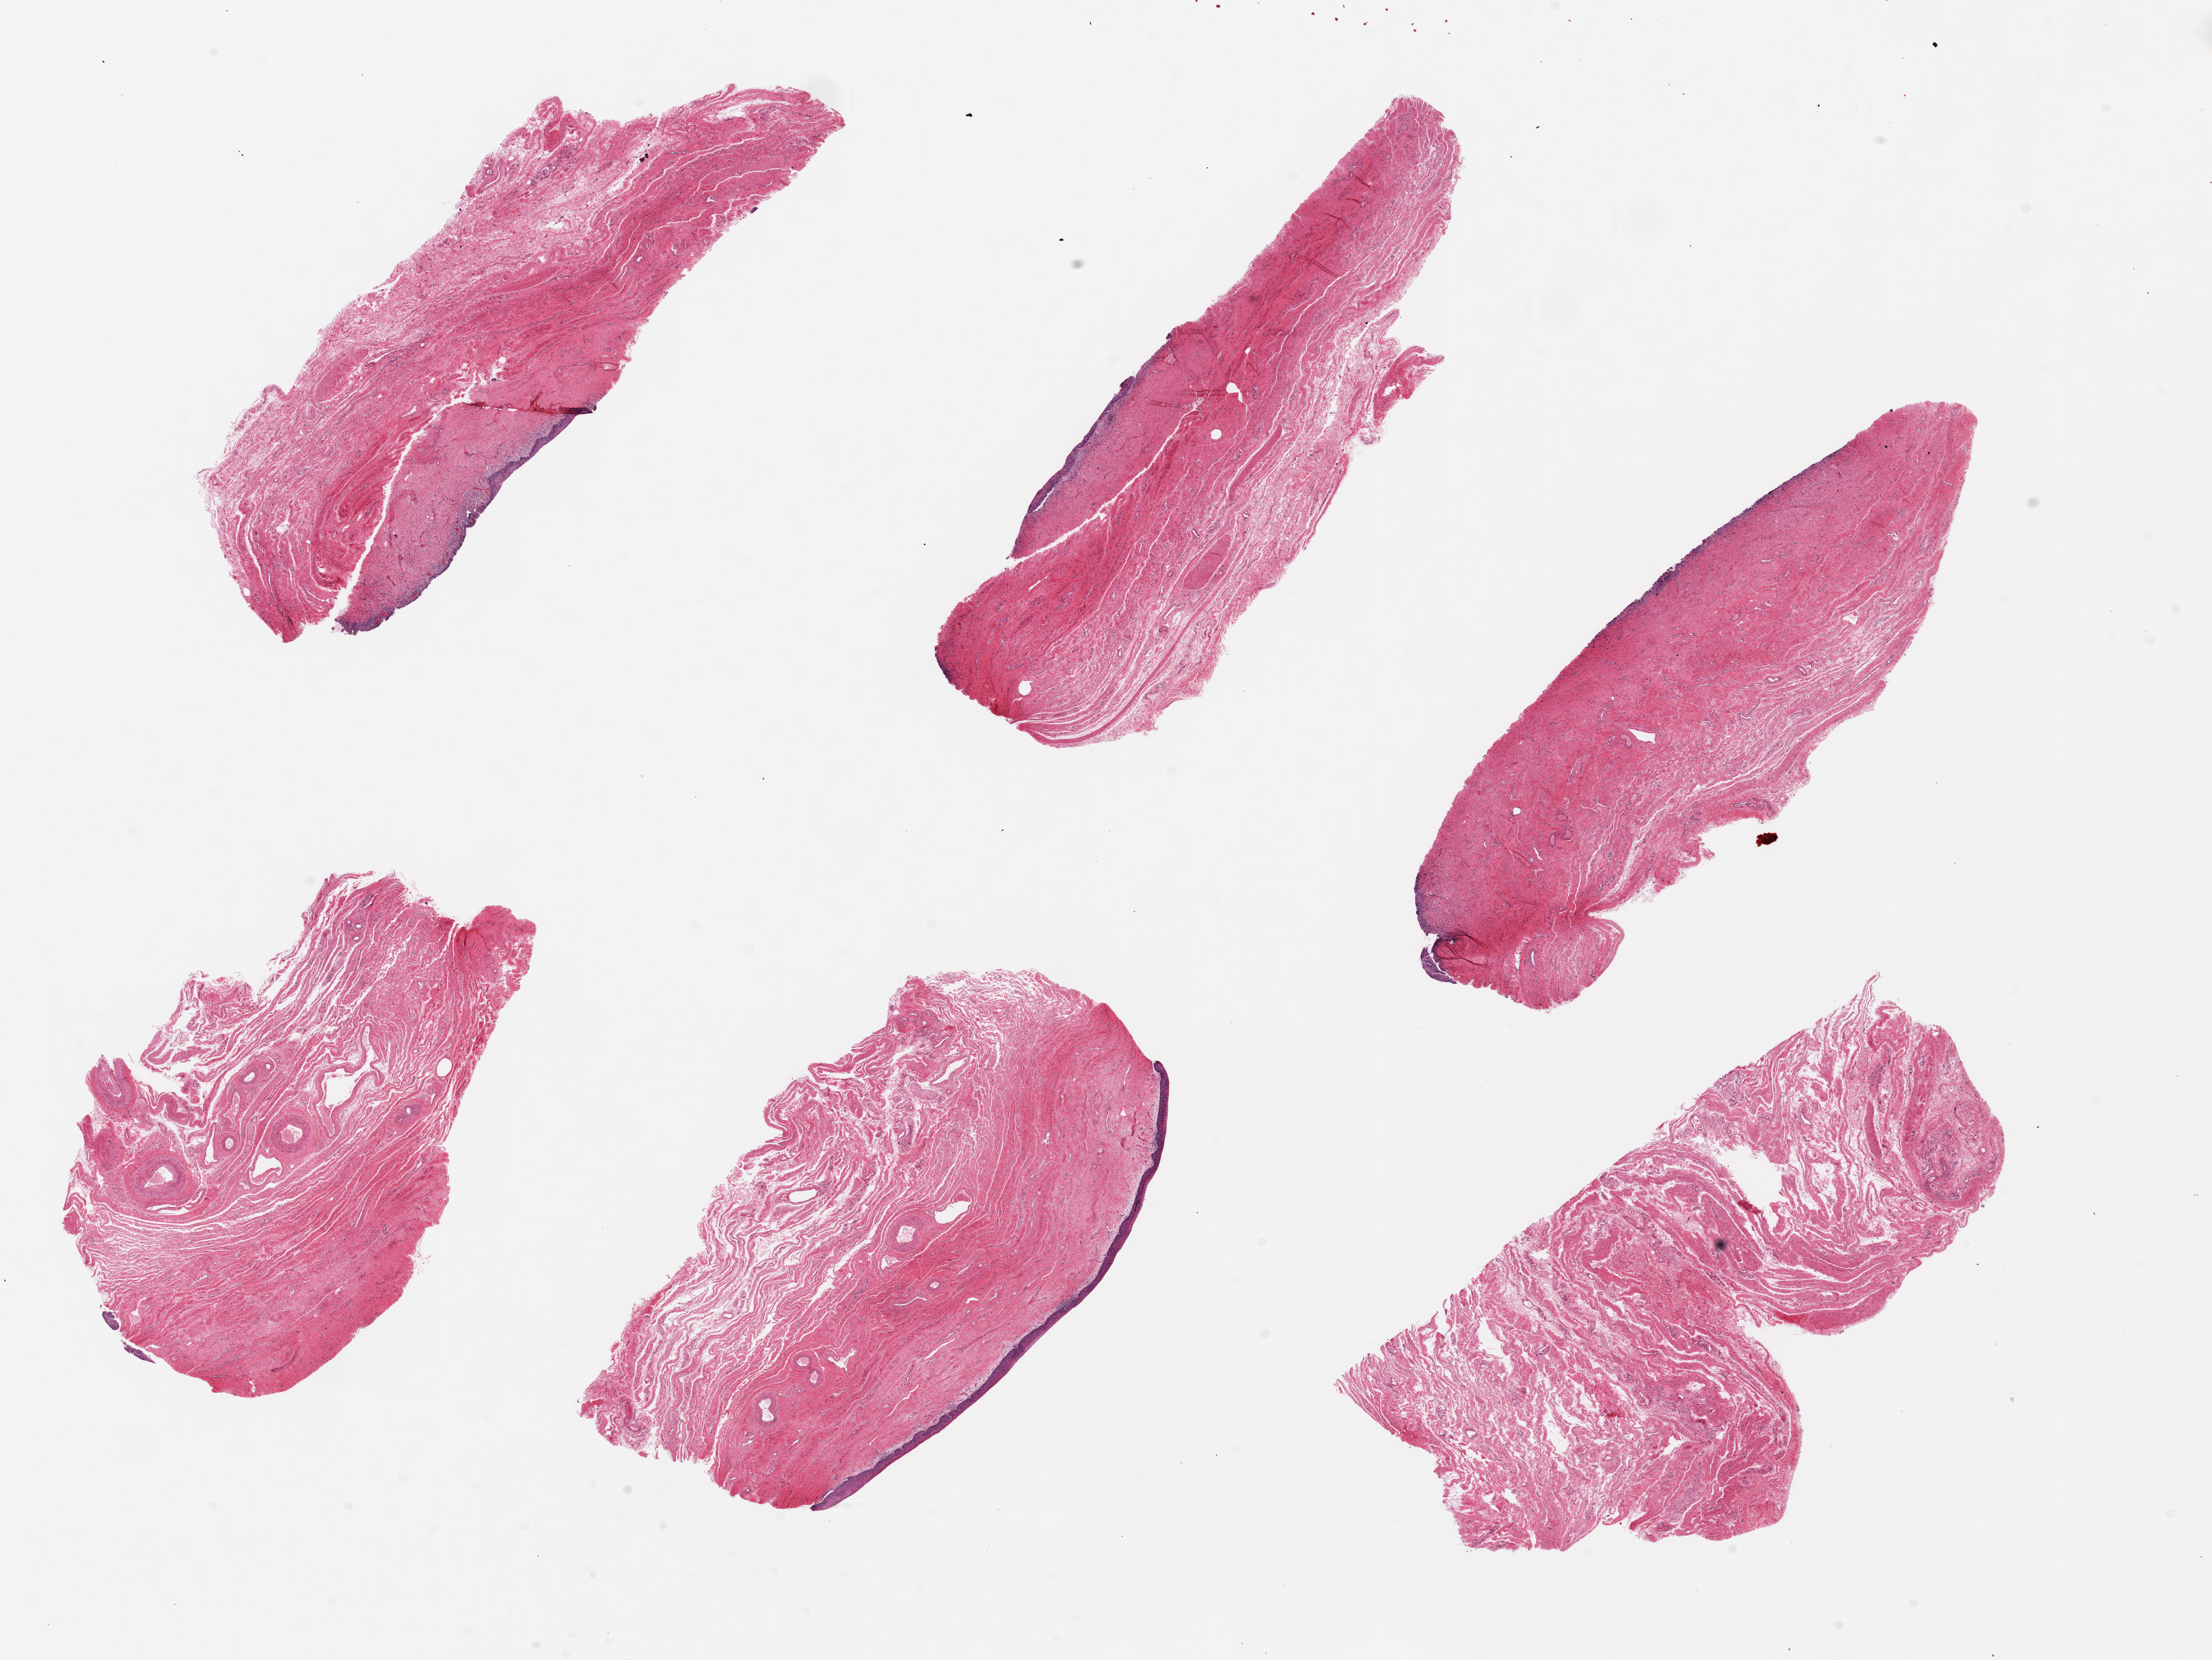
Digitized H&E-stained section — a low-resolution overview of the entire scanned area, about 25.6 x 19.2 mm. PAXgene-fixed, paraffin-embedded tissue. Section of vagina (target tissue). Donor tissue sample. Donor: female.
Pathologist's review note for this sample: 6 pieces, up to 9x3mm; moderate chronic inflammation; >60% sloughed epithelium; good mucosa in 1 piece.